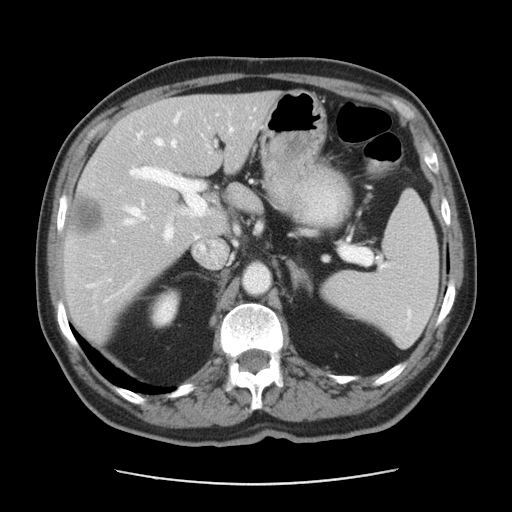
Contrast-enhanced abdominal CT, one axial slice; reconstruction kernel STANDARD; intravenous contrast given; soft-tissue window (W 400 / L 40 HU); 5 mm slice thickness; 512 × 512 image matrix. Male patient, age 73 years. From the clinical record (not read from this slice): diagnosis: colorectal cancer liver metastases, imaged before liver resection; multiple liver metastases: yes; largest metastasis: 0.5 cm.
Outlined on this slice (outlined manually by an expert reader):
- hepatic veins: box from (x=86, y=117) to (x=178, y=288) px
- liver: (x=64, y=94)–(x=275, y=337)
- planned liver remnant (the part of the liver to remain after resection): (x=110, y=95)–(x=275, y=236)
- portal vein (with intrahepatic branches): (x=130, y=132)–(x=205, y=239)
- liver metastasis: (x=71, y=197)–(x=104, y=234)